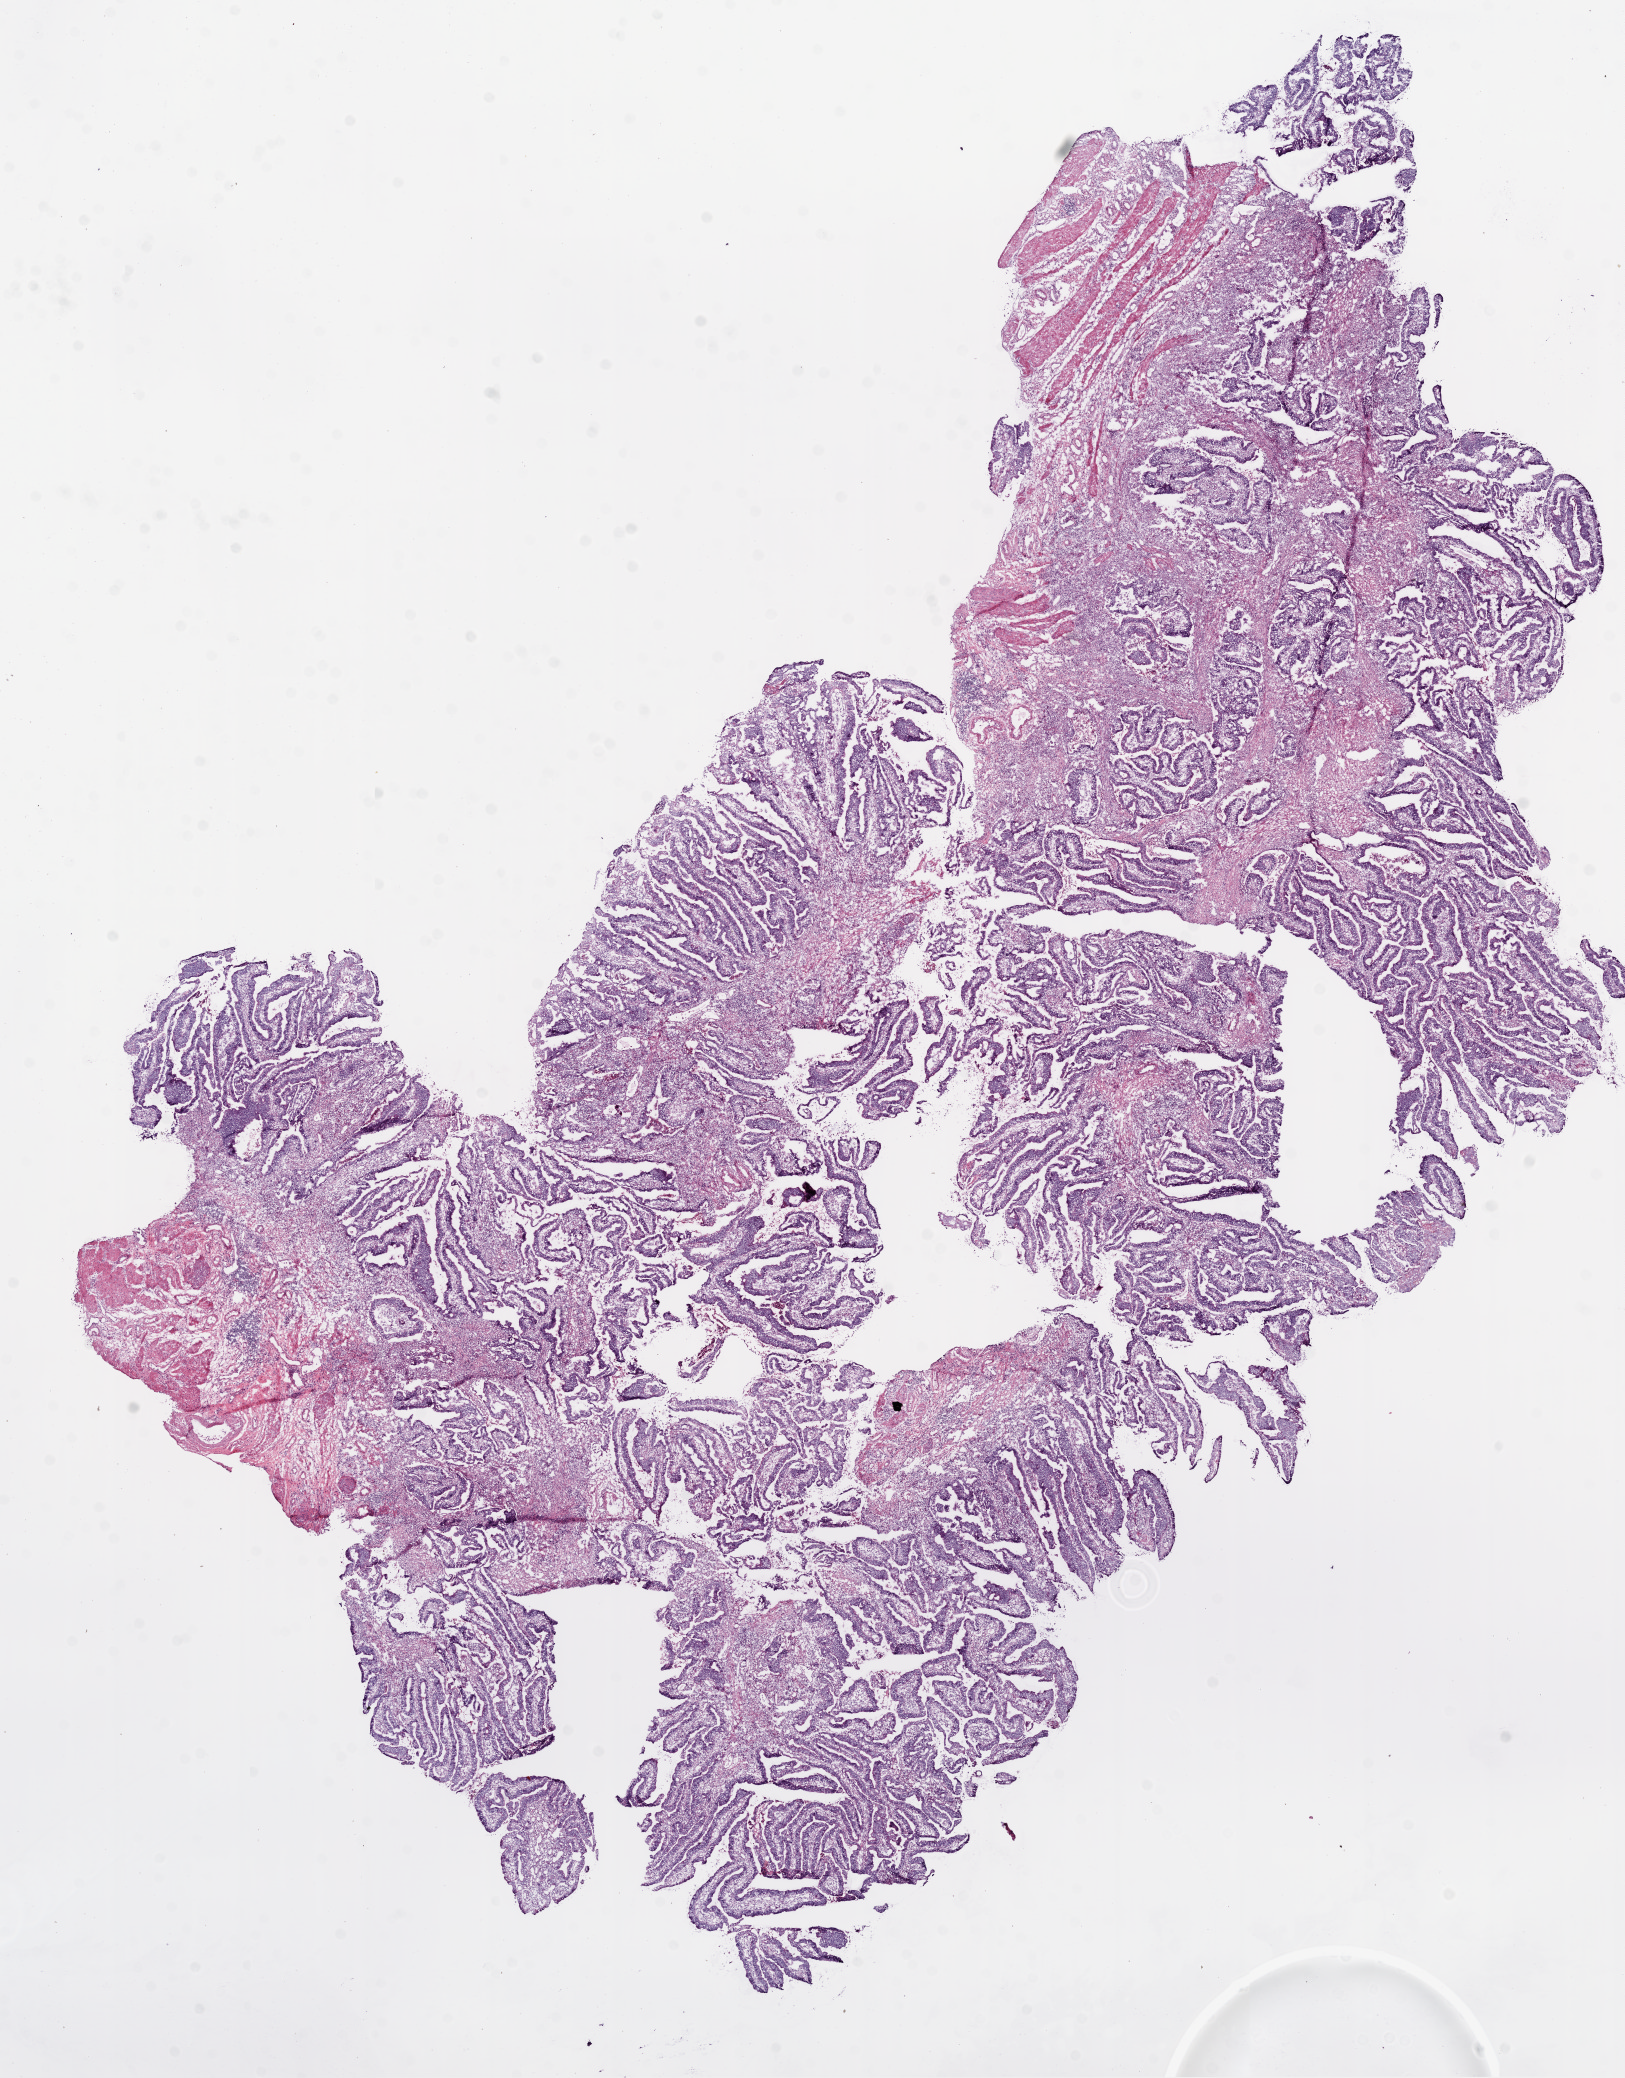
H&E whole-slide image, shown as a low-resolution overview of the whole scanned area (about 13.0 x 16.7 mm); frozen section from the bottom of the tissue portion; colon, primary tumour sample. Male, age 69 years at initial diagnosis. Pathologist review of this section (percent, as recorded): tumour cells 70%, tumour nuclei 75%, normal cells 10%, stromal cells 15%, necrosis 5%.
AJCC pathologic stage: I. Pathologic diagnosis: Adenocarcinoma, NOS (cecum). Lymph nodes positive (case pathology): 0 of 28 examined.